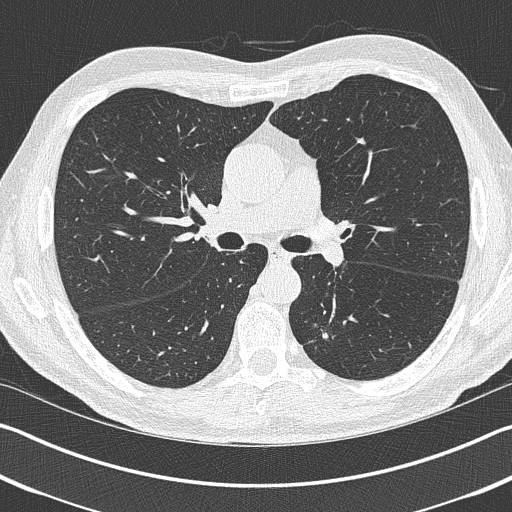
Low-dose screening chest CT, one axial slice; slice 249 of 402 in the series (ordered by position); lung window (W 1500 / L -600 HU); 1 mm slice thickness; 512 × 512 image matrix, field of view 340 × 340 mm.
Annotated regions visible in this slice (outlined manually by an expert reader):
- lesion 1 (tumor, lower lobe of left lung): box from (x=322, y=333) to (x=328, y=339) px